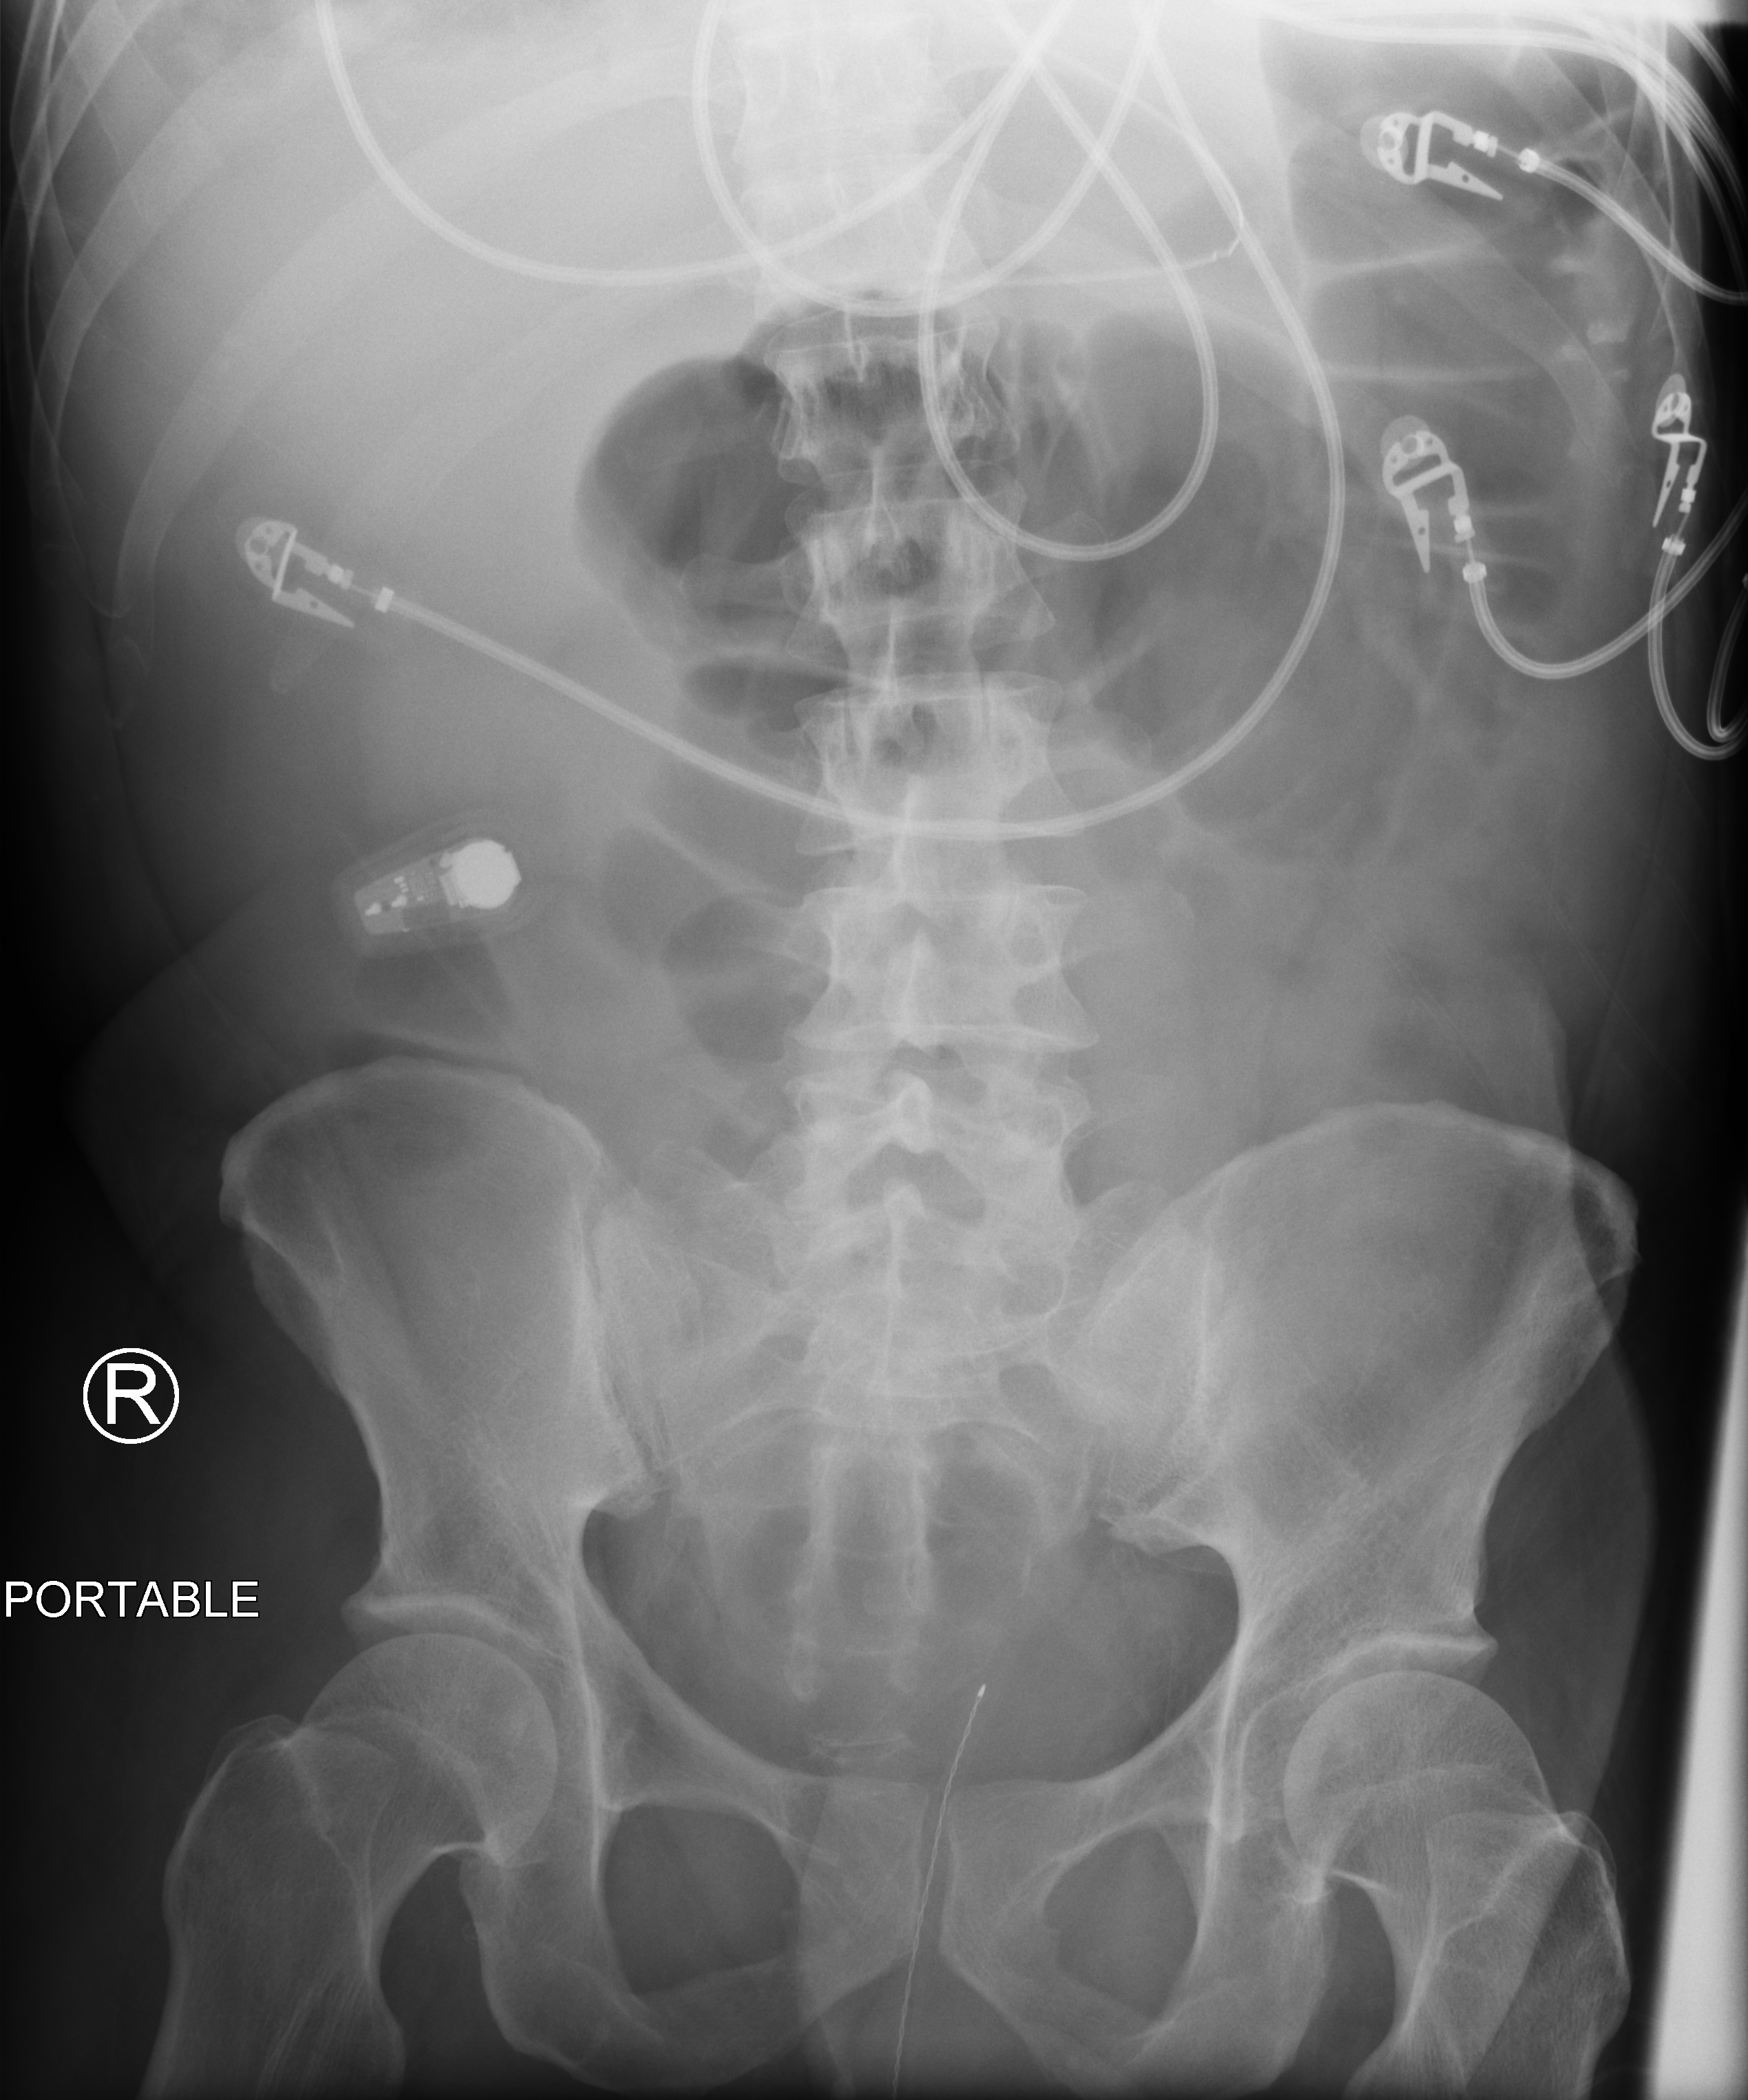
Abdomen X-ray (portable). Male patient hospitalised with COVID-19, age 18–59 years.
Hospital-stay facts (about this admission, not read from this image; timing relative to this image not recorded): chronic kidney disease (admission record): no; admitted to intensive care during this hospital stay: yes; length of hospital stay: 96 days.